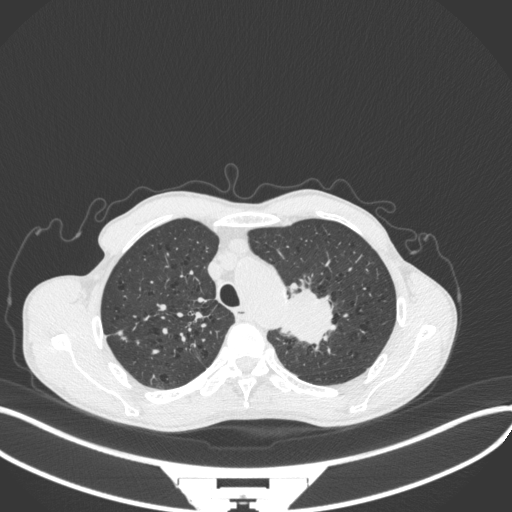
Chest CT, one axial slice; slice 328 of 394 in the series (ordered by position); 120 kVp; lung window (W 1500 / L -600 HU); 1 mm slice thickness; 512 × 512 image matrix, field of view 400 × 400 mm. Patient: male, 65 years. From the clinical record (not read from this slice): clinical TNM (as recorded): T2b N0 M0; histopathological grade: G2.
Annotated regions visible in this slice (rectangle marked by the reading radiologist):
- lung tumour (recorded histology: adenocarcinoma): bounding box (x1, y1, x2, y2) in pixels: (276, 274, 341, 351)